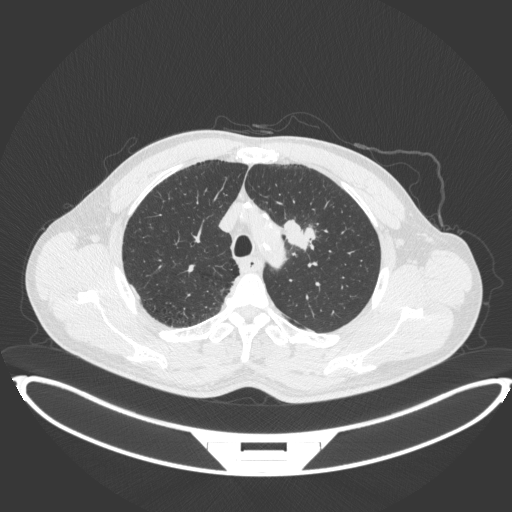
Chest CT, one axial slice. Position 337 of 407 along the scan axis. Reconstruction kernel B31f. 120 kVp. Lung window (W 1500 / L -600 HU). 1 mm slice thickness. 512 × 512 image matrix, field of view 457 × 457 mm. Patient: male, 60 years. Case-level facts recorded for this patient, not image findings: clinical TNM (as recorded): T2a N0 M0; histopathological grade: G1-G2.
Structures marked on this image (bounding box drawn by a radiologist):
- lung tumour (recorded histology: squamous cell carcinoma): bounding box <282,217,318,253> (left, top, right, bottom; pixels)